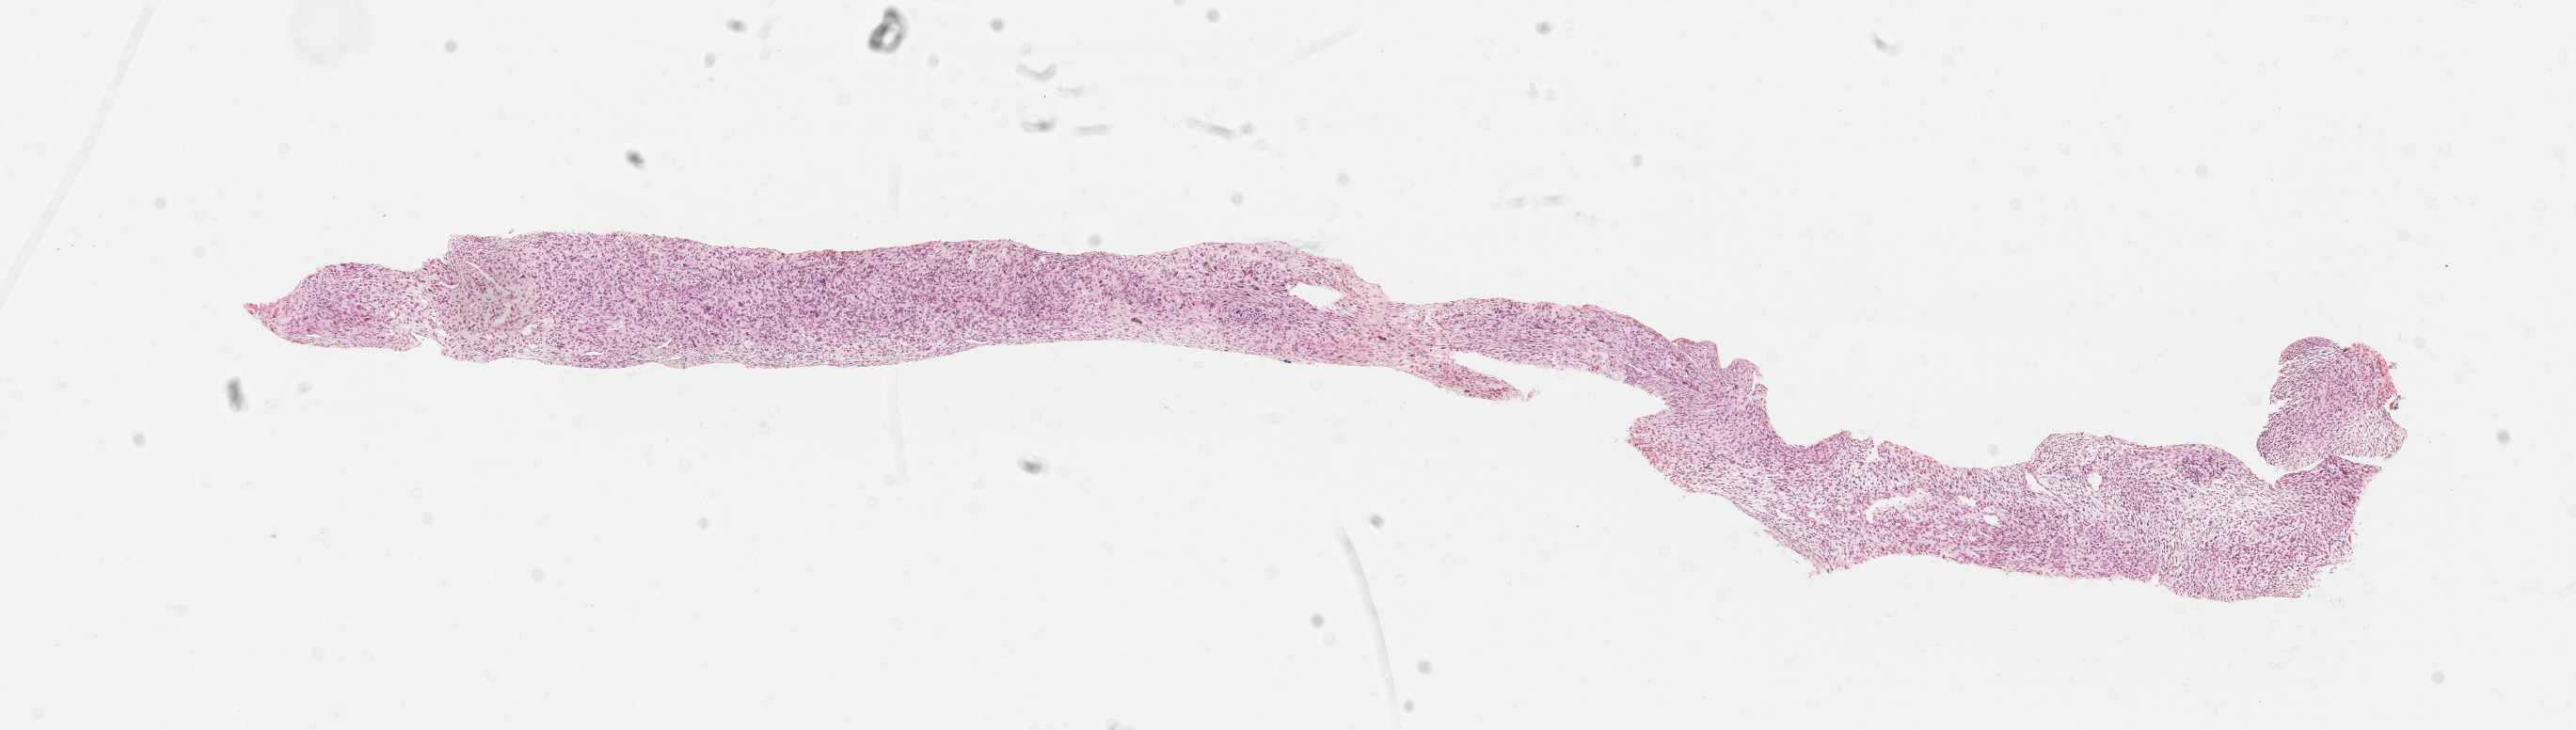
Whole-slide image, H&E stain of tumor tissue — a low-resolution overview of the entire scanned area, about 11.1 x 3.1 mm; FFPE section; site: retroperitoneum. Patient: male, age 3.4 years at diagnosis.
Diagnosis: rhabdomyosarcoma; histological classification: embryonal rhabdomyosarcoma.